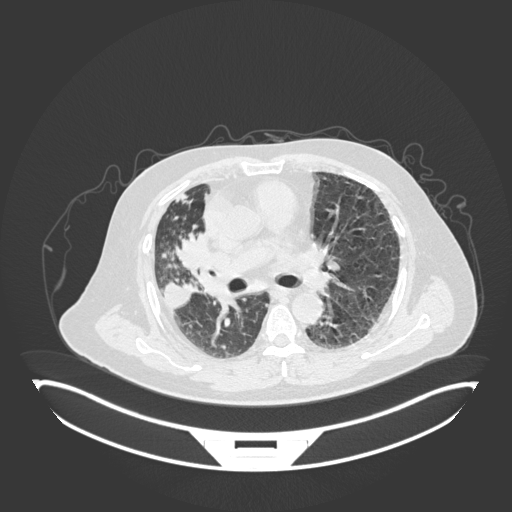
Chest CT, one axial slice. Slice 91 of 201 in the series (ordered by position). Reconstruction kernel B30f. 120 kVp. Lung window (W 1500 / L -600 HU). 512 × 512 image matrix, field of view 500 × 500 mm. Patient: male, 69 years. From the clinical record (not read from this slice): clinical TNM (as recorded): T4 N3 M1.
Annotated regions visible in this slice (bounding box drawn by a radiologist):
- lung tumour (recorded histology: adenocarcinoma): bounding box (x1, y1, x2, y2) in pixels: (174, 234, 215, 275)